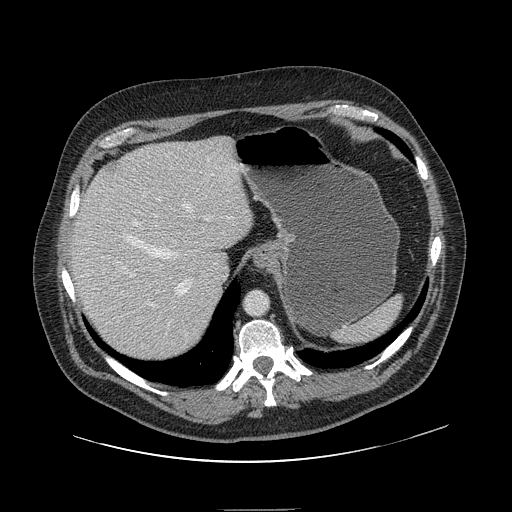
Contrast-enhanced abdominal CT, one axial slice; position 114 of 154 along the scan axis; soft-tissue window (W 400 / L 40 HU); 2.5 mm slice thickness; 512 × 512 image matrix. Male patient, age 61 years. From the clinical record (not read from this slice): diagnosis: colorectal cancer liver metastases, imaged before liver resection; multiple liver metastases: yes.
Outlined on this slice (outlined manually by an expert reader):
- hepatic veins: bounding box (x1, y1, x2, y2) in pixels: (125, 202, 194, 294)
- liver: (71, 138, 253, 362)
- planned liver remnant (the part of the liver to remain after resection): (72, 144, 253, 356)
- portal vein (with intrahepatic branches): (122, 198, 211, 306)